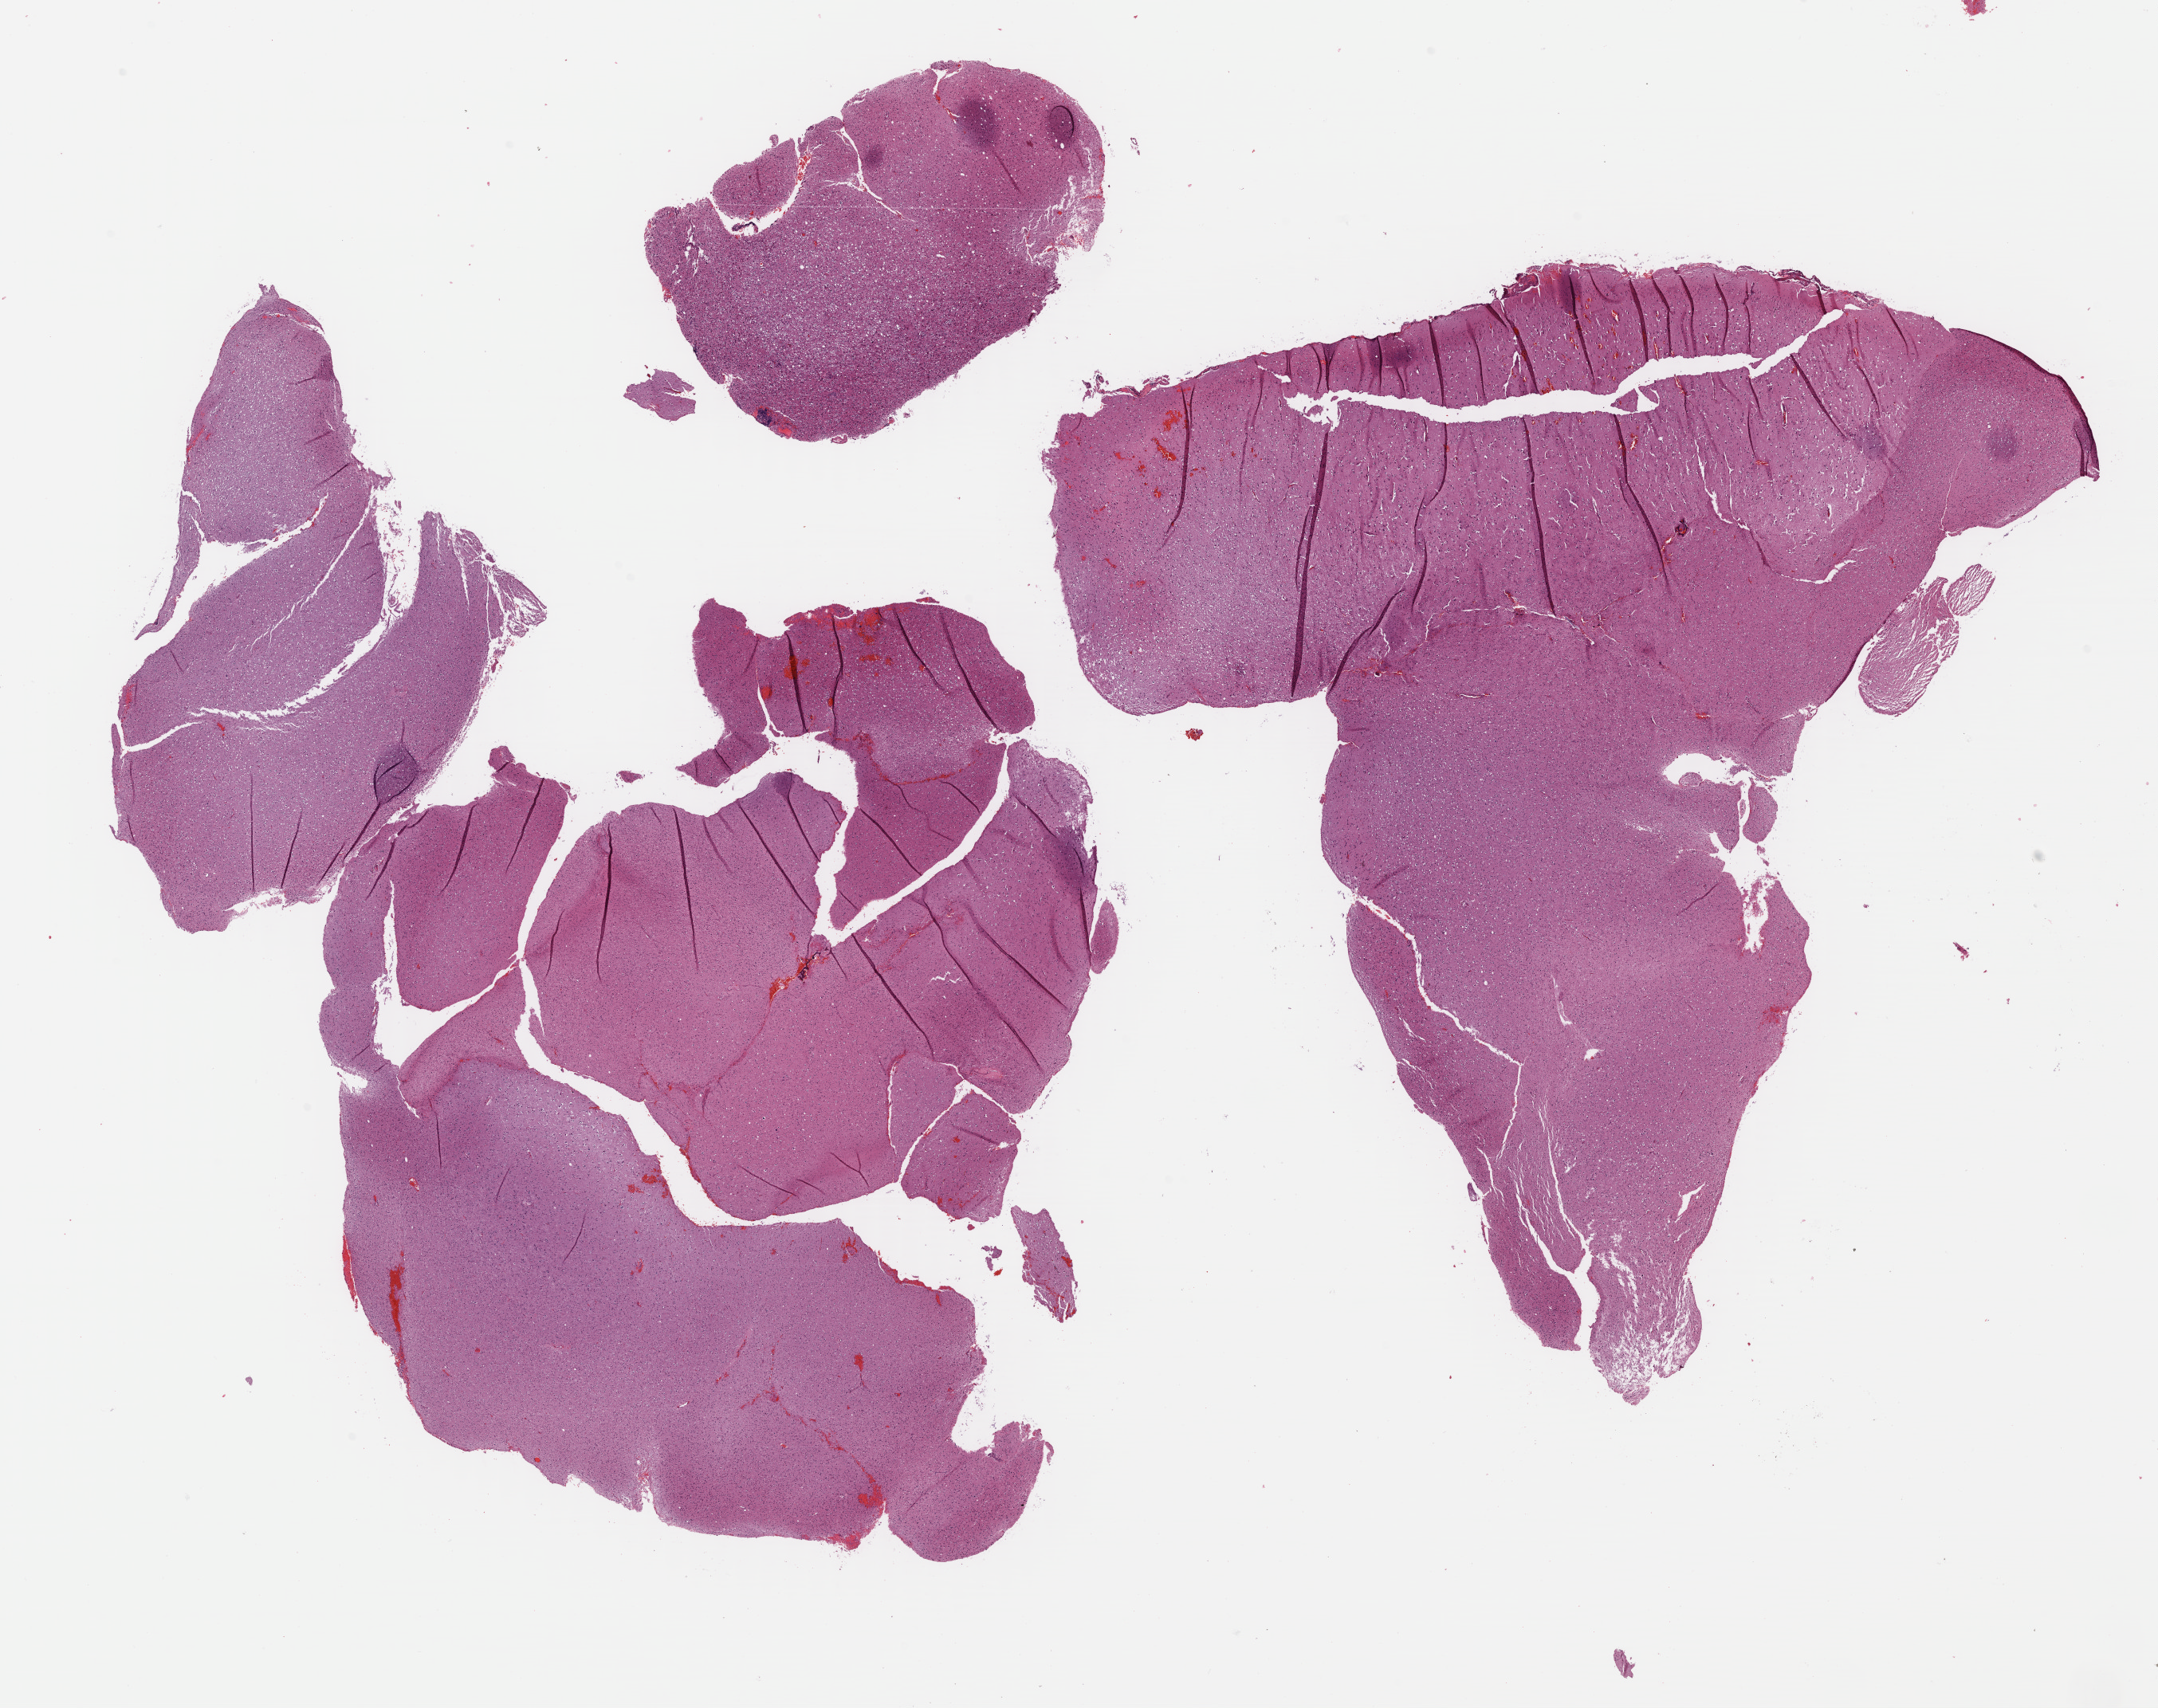
Whole-slide histology image, H&E — shown as a low-resolution overview of the whole scanned area (about 21.3 x 16.8 mm, from a 40x scan), FFPE section, brain, primary tumour sample. Patient: male, age at initial diagnosis 44 years. Histologic grade: G3 (poorly differentiated).
Laterality: right. Histologic diagnosis: Astrocytoma, anaplastic.